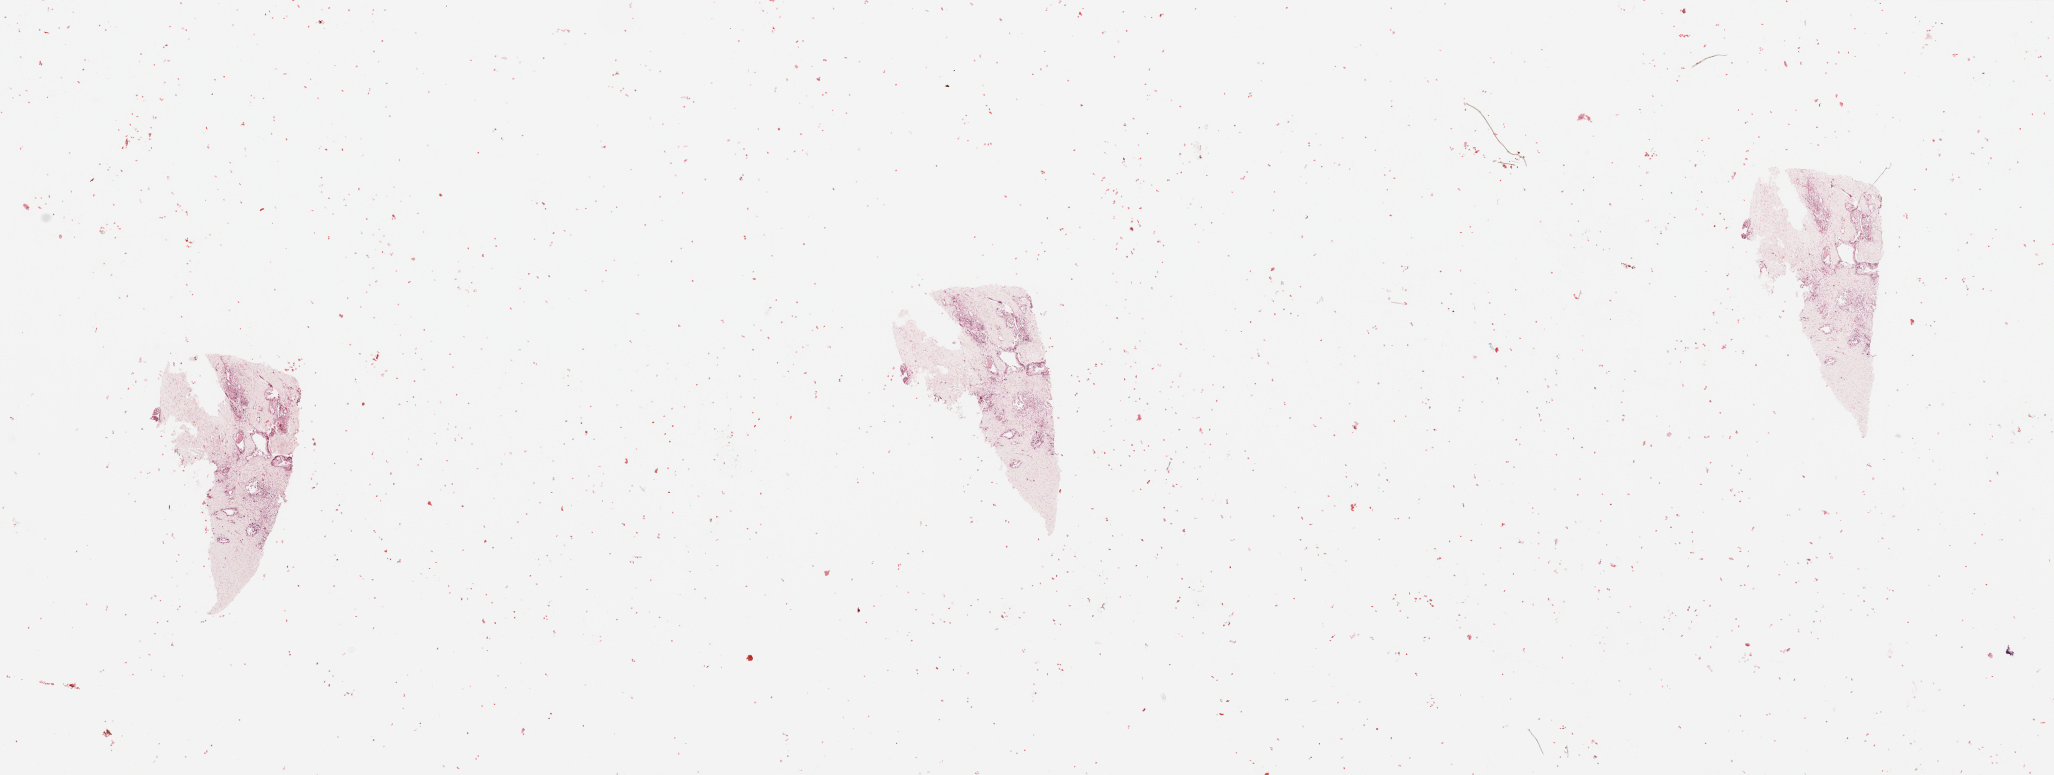
Digitized H&E-stained tissue section (whole slide) — whole scanned area (about 32.5 x 12.3 mm) shown as a low-resolution overview. Tumour tissue sample, sampled site: pancreas. Patient: male, age 56 years. Histologic grade: G2 (moderately differentiated). Composition of this section per pathologist review: tumour nuclei 30%, necrosis 1%.
AJCC pathologic stage: IV. Diagnosis: Infiltrating duct carcinoma, NOS. Primary tumour site (as recorded): head.